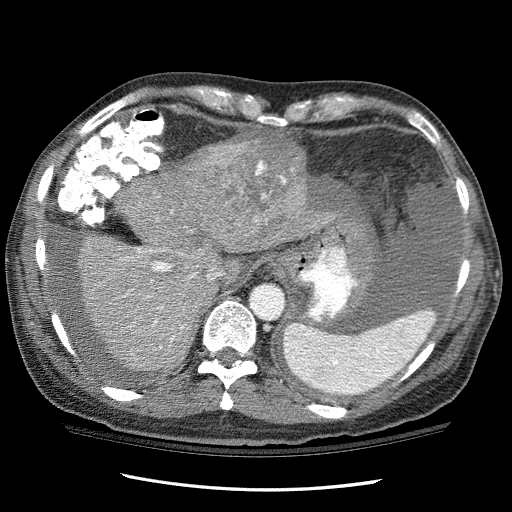
Contrast-enhanced abdominal CT (liver protocol), one axial slice; reconstruction kernel STANDARD; one of 3 acquisitions stored at this slice position; soft-tissue window (W 400 / L 40 HU); 512 × 512 image matrix, field of view 360 × 360 mm. From the clinical record (not read from this slice): diagnosis: hepatocellular carcinoma (patient treated with transarterial chemoembolisation; whether this scan precedes or follows treatment is not stated here); TNM stage (as recorded): Stage-I; Child-Pugh class: C; tumour differentiation: well differentiated; tumour nodularity: uninodular.
Structures marked on this image (semi-automatic segmentation, software-assisted and operator-edited):
- abdominal aorta: bounding box <251,285,284,319> (left, top, right, bottom; pixels)
- liver parenchyma outside the tumour (the mass and vessels are separate outlines, so this box may not span the whole liver): <77,152,330,370>
- mass: <187,131,310,246>
- liver vessels: <123,248,222,348>